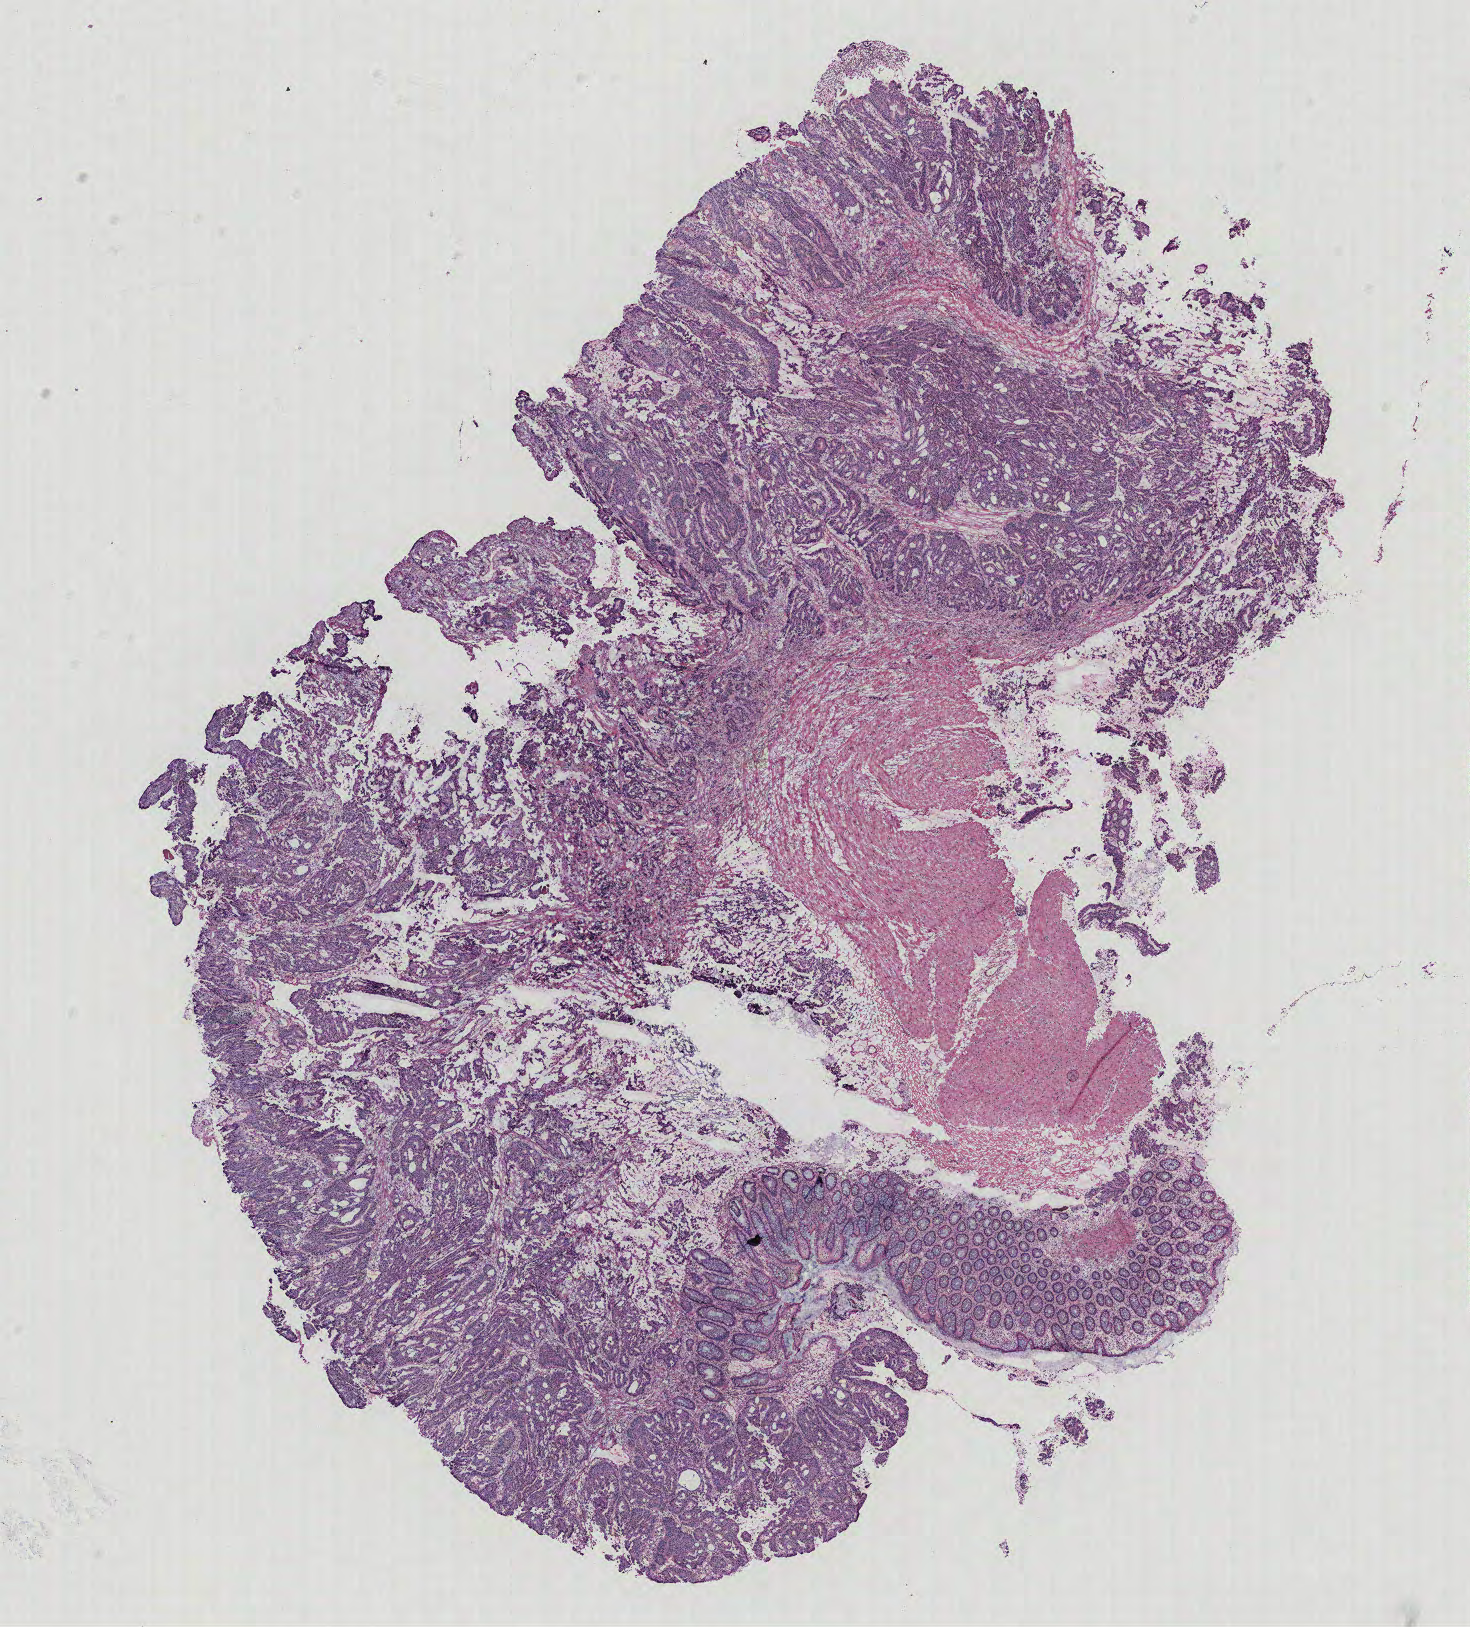
Digitized H&E-stained tissue section (whole slide) — shown as a low-resolution overview of the whole scanned area (about 11.8 x 13.0 mm). Colon, tissue type not recorded. Female patient.
- patient diagnosis: Adenocarcinoma, NOS